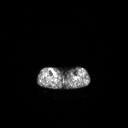
FDG PET of an extremity soft-tissue mass (from a PET/CT study), one axial slice; position 130 of 267 along the scan axis; 128 × 128 image matrix. Patient: female, 65 years. From the clinical record (not read from this slice): histological type: undifferentiated – high grade; grade: high; site of the primary tumour: right thigh.
Outlined on this slice (expert contour drawn on MRI and transferred to this co-registered scan by the dataset authors):
- gross tumour volume (mass): box from (x=51, y=69) to (x=54, y=72) px